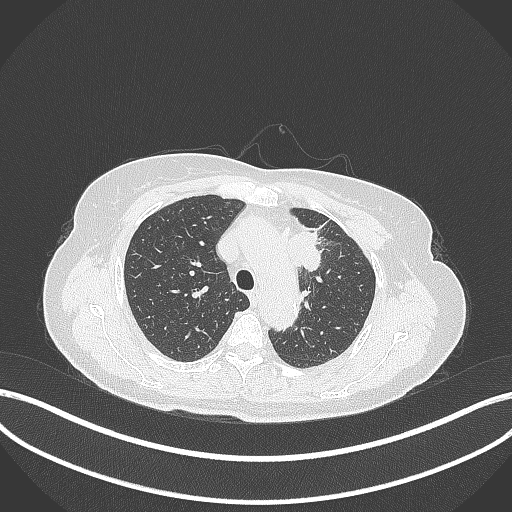
Chest CT, one axial slice. Position 248 of 369 along the scan axis. 120 kVp. Lung window (W 1500 / L -600 HU). 1 mm slice thickness. 512 × 512 image matrix. Female patient, age 65 years. Case-level facts recorded for this patient, not image findings: clinical TNM (as recorded): T2a N0 M0; histopathological grade: G2-3.
Outlined on this slice (rectangle marked by the reading radiologist):
- lung tumour (recorded histology: adenocarcinoma): bounding box (x1, y1, x2, y2) in pixels: (284, 228, 324, 273)